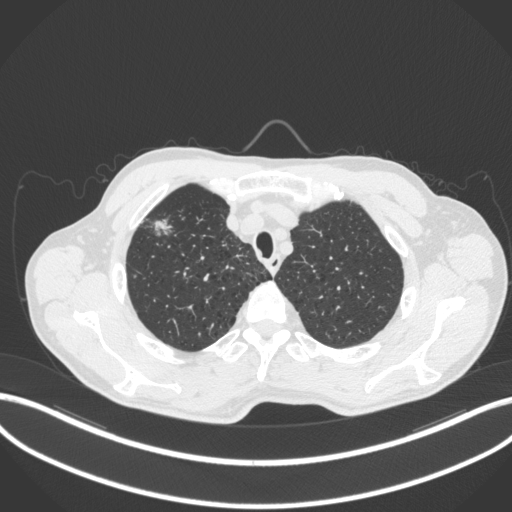
Chest CT, one axial slice. Slice 355 of 414 in the series (ordered by position). Lung window (W 1500 / L -600 HU). 1 mm slice thickness. 512 × 512 image matrix, field of view 400 × 400 mm. Patient: male, 69 years. From the clinical record (not read from this slice): clinical TNM (as recorded): T1b N1 M0.
Structures marked on this image (bounding box drawn by a radiologist):
- lung tumour (recorded histology: adenocarcinoma): bounding box [x1, y1, x2, y2] px = [150, 214, 177, 235]